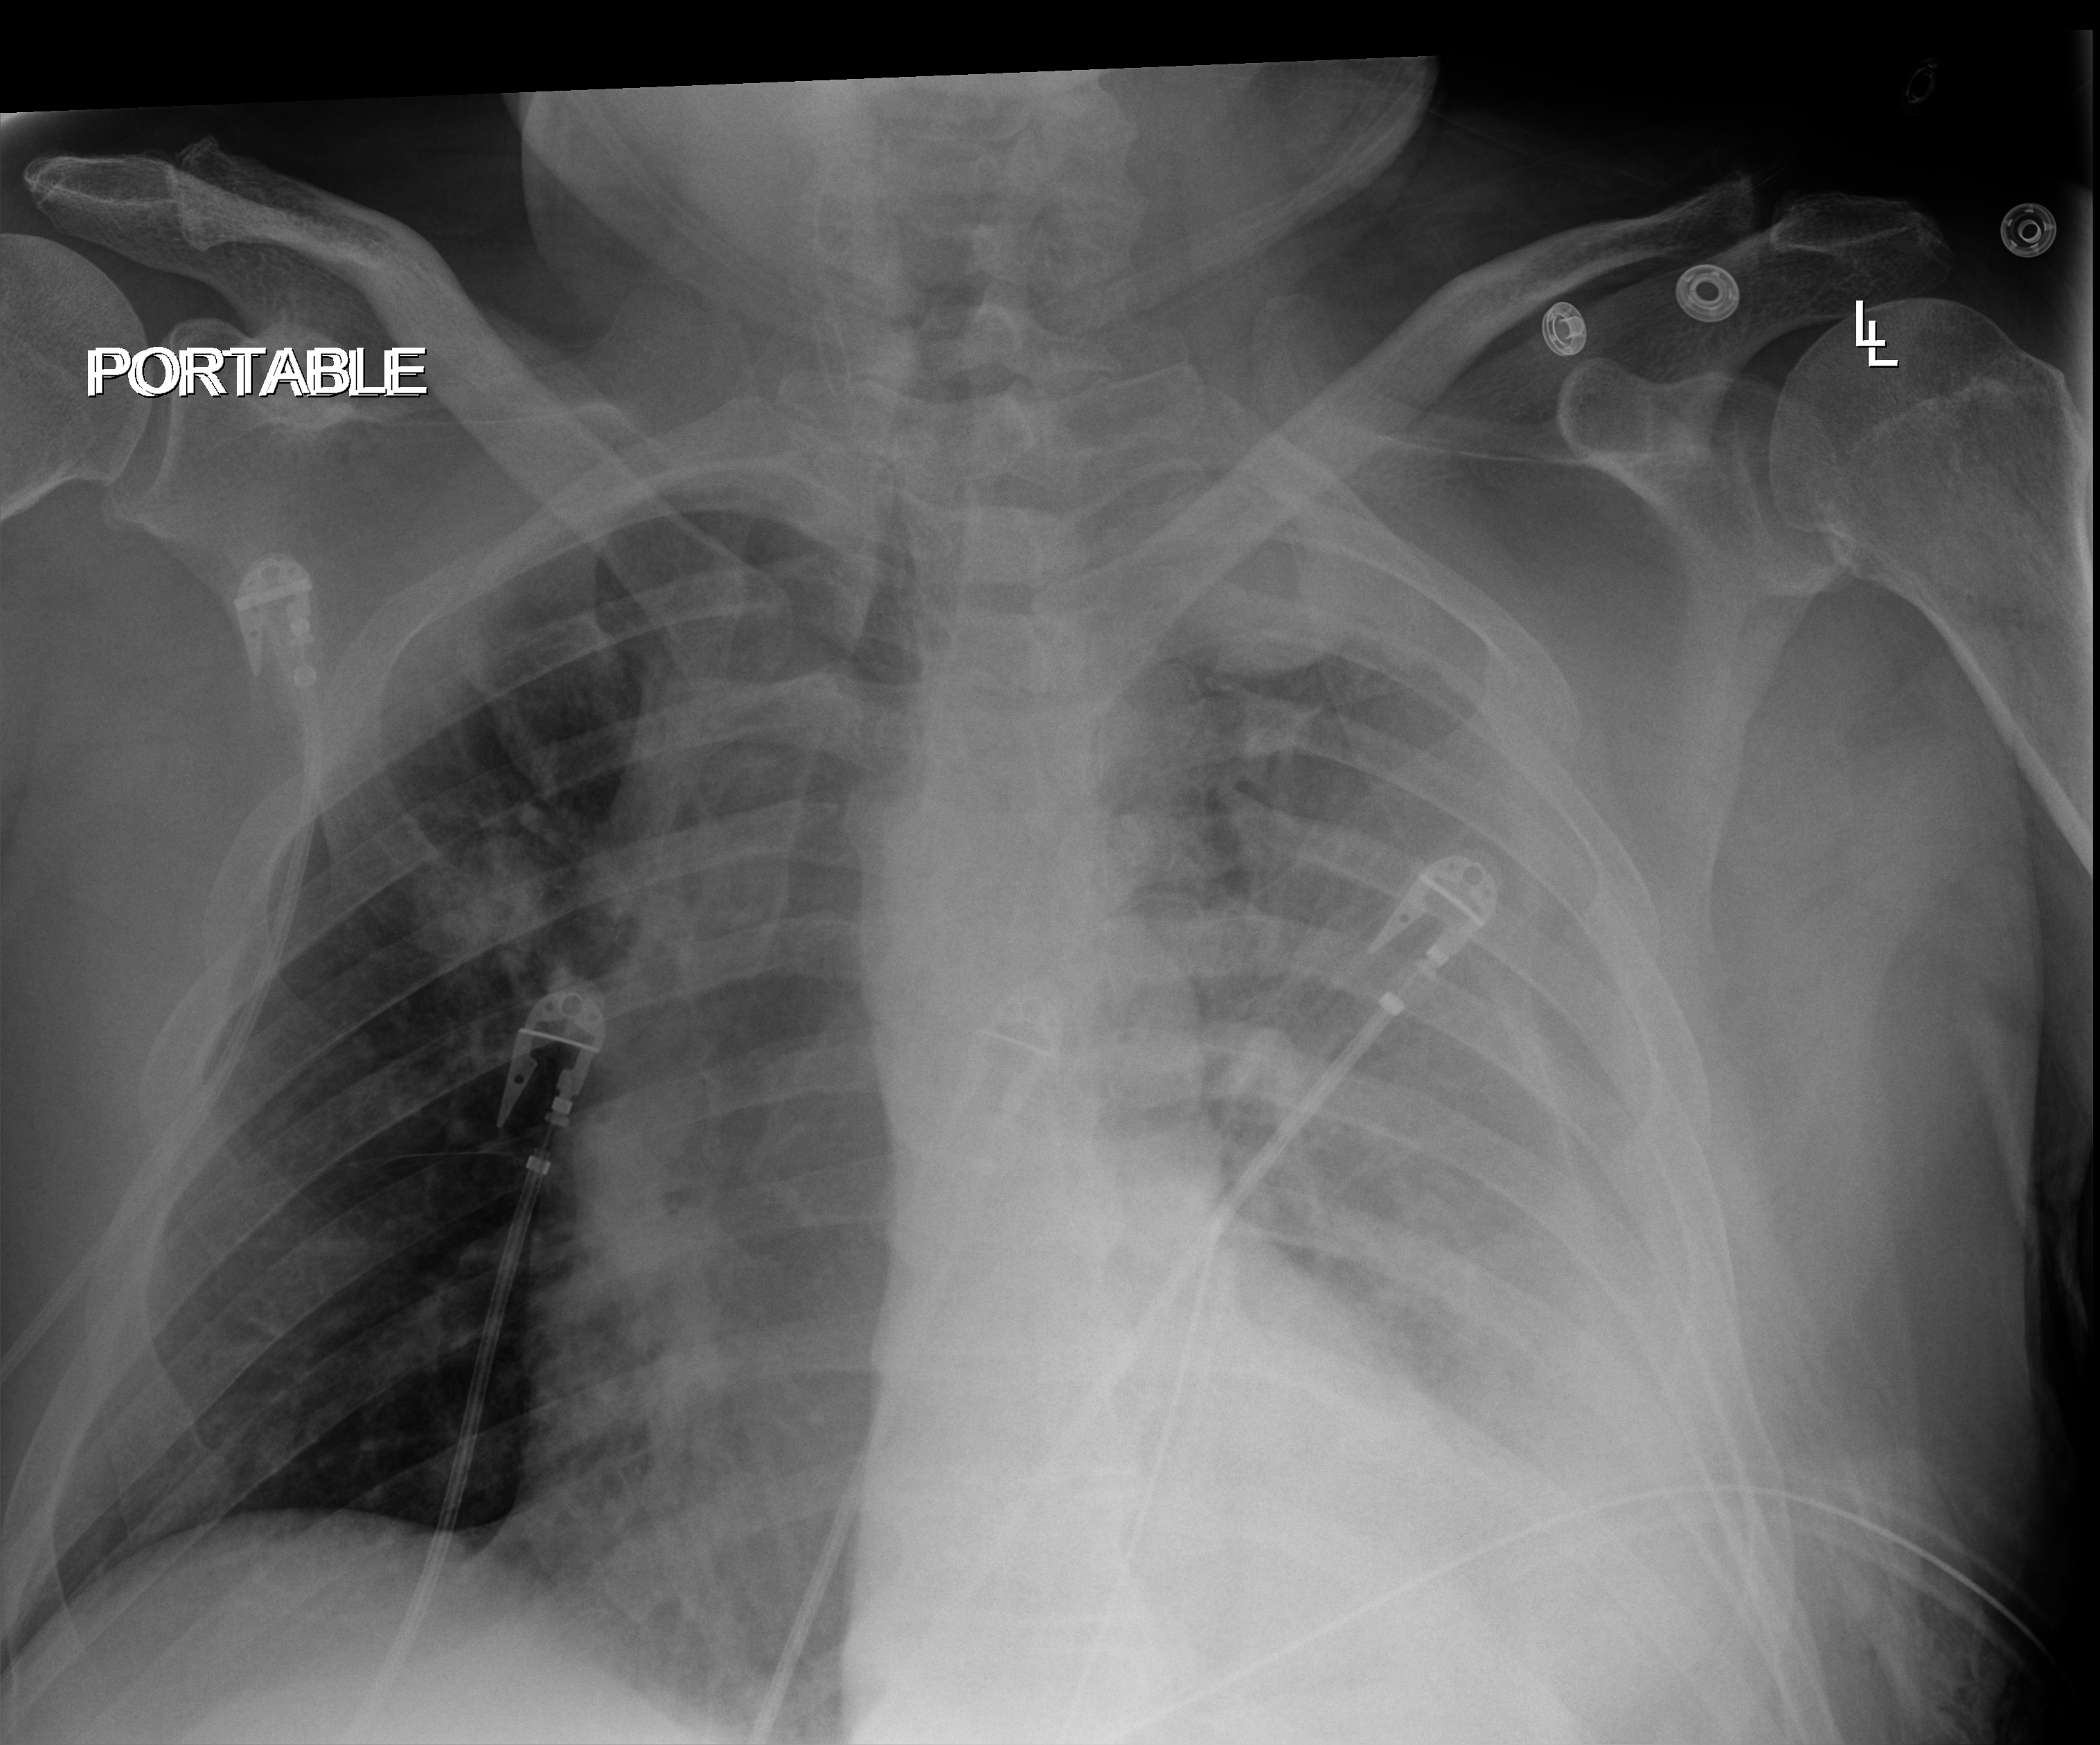
Portable chest radiograph; anteroposterior (AP) projection. Male patient hospitalised with COVID-19, age 18–59 years.
From the hospital-stay record, not from the radiograph (when in the stay this image was taken is not recorded):
- mechanically ventilated during this hospital stay: no
- admitted to intensive care during this hospital stay: no